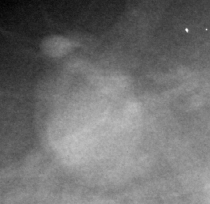
Region of interest cut from a scanned film mammogram (one marked finding); right breast; CC view.
Finding: mass, shape oval / lymph node, margins circumscribed; BI-RADS assessment category 2; subtlety rating 4 on a 1 (subtle) to 5 (obvious) scale; benign without callback (not worked up further).